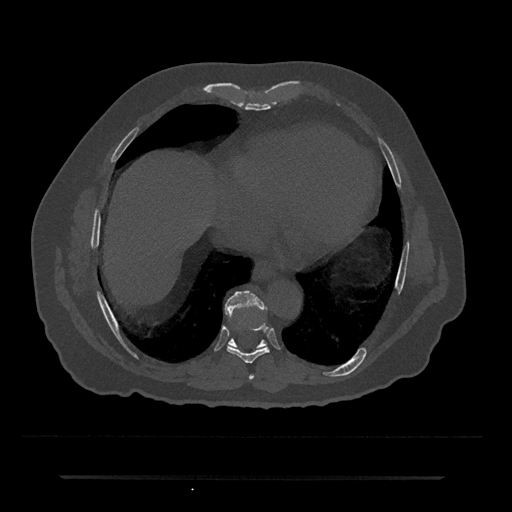
CT including the spine, one axial slice; slice 315 of 797 in the series (ordered by position); reconstruction kernel Br40s/3; 120 kVp; bone window (W 1800 / L 400 HU); 0.5 mm slice thickness; 512 × 512 image matrix. Patient: male, 69 years. Case-level facts recorded for this patient, not image findings: primary cancer: prostate.
Structures marked on this image (semi-automatic segmentation, software-assisted and operator-edited):
- T7 vertebra: bounding box [x1, y1, x2, y2] px = [249, 374, 255, 380]
- T8 vertebra: [227, 323, 270, 364]
- T9 vertebra: [225, 290, 267, 345]